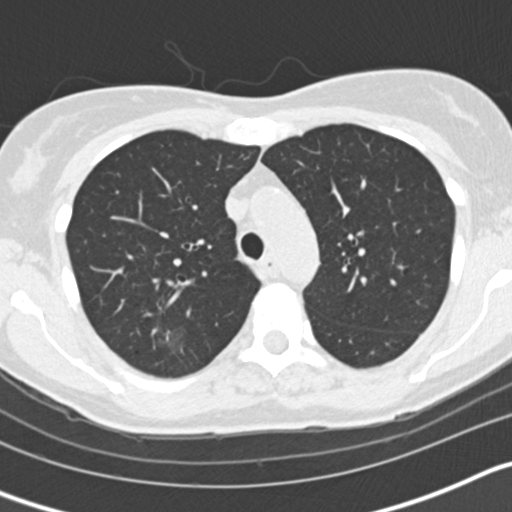
Chest CT (low-dose screening protocol), one axial image. Second screening round (one year after baseline). Lung window (W 1500 / L -600 HU). Slice 48 of 163 in the series. Female, age 58 years at enrolment. Current smoker at enrolment.
Expert-annotated lung lesion, box from (x=138, y=316) to (x=199, y=368) px. The screening reader recorded 3 non-calcified nodules or masses ≥4 mm on this exam (right upper lobe, left upper lobe, left lower lobe); which of them this box marks is not recorded. Later outcome: lung cancer diagnosed 59 days after this screen — bronchiolo-alveolar adenocarcinoma, NOS, right upper lobe, moderately differentiated (G2), stage IA (AJCC 6th edition), 7 mm at pathology.